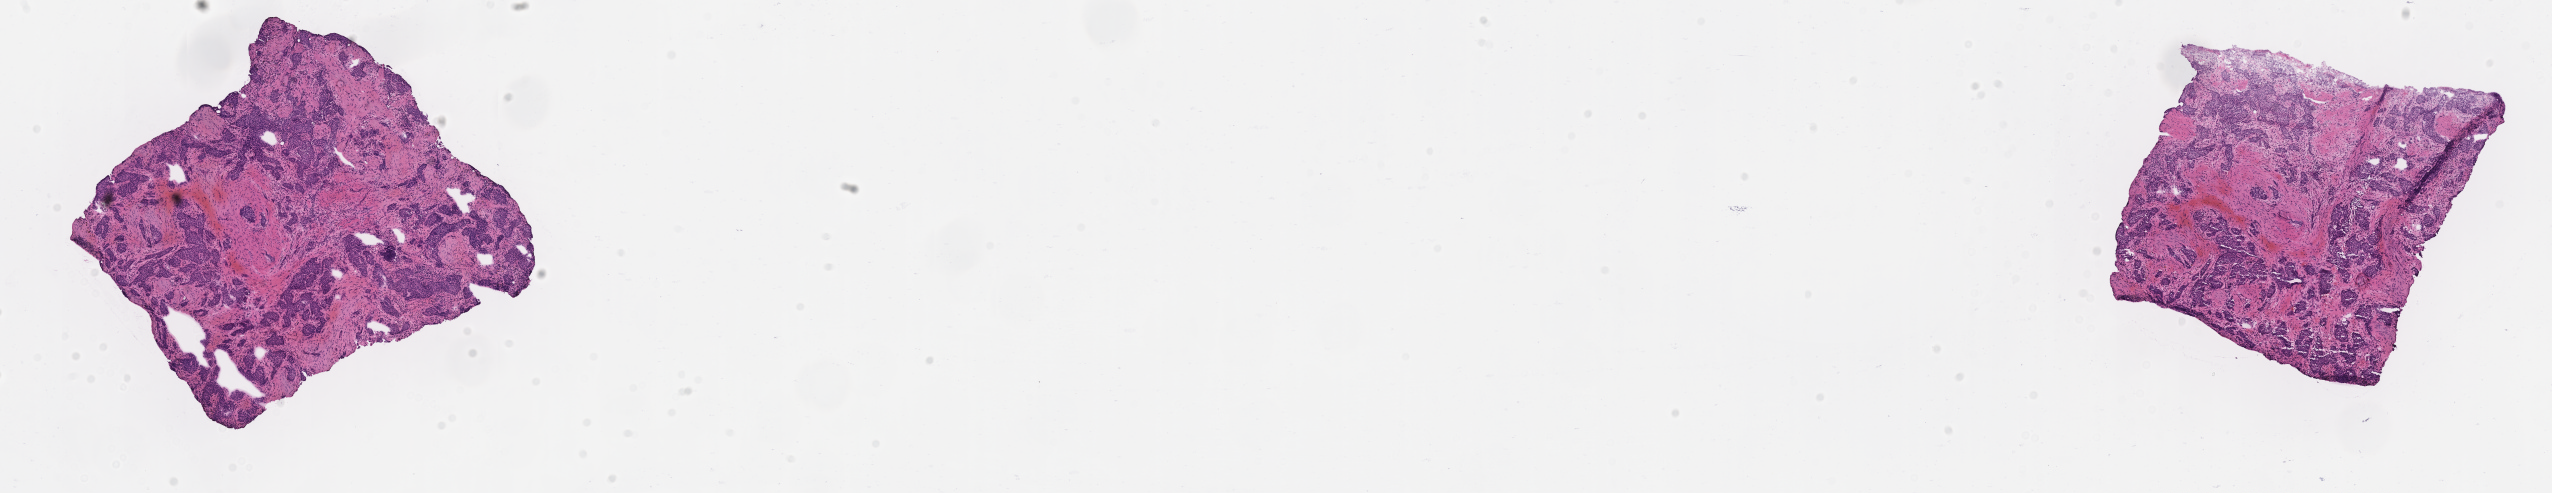
Haematoxylin and eosin whole-slide image — a low-resolution overview of the entire scanned area, about 20.6 x 4.0 mm, frozen section, primary tumor, anatomic site: breast (left). Patient: female, age at initial diagnosis 42 years.
Histologic diagnosis: Infiltrating duct carcinoma, NOS.